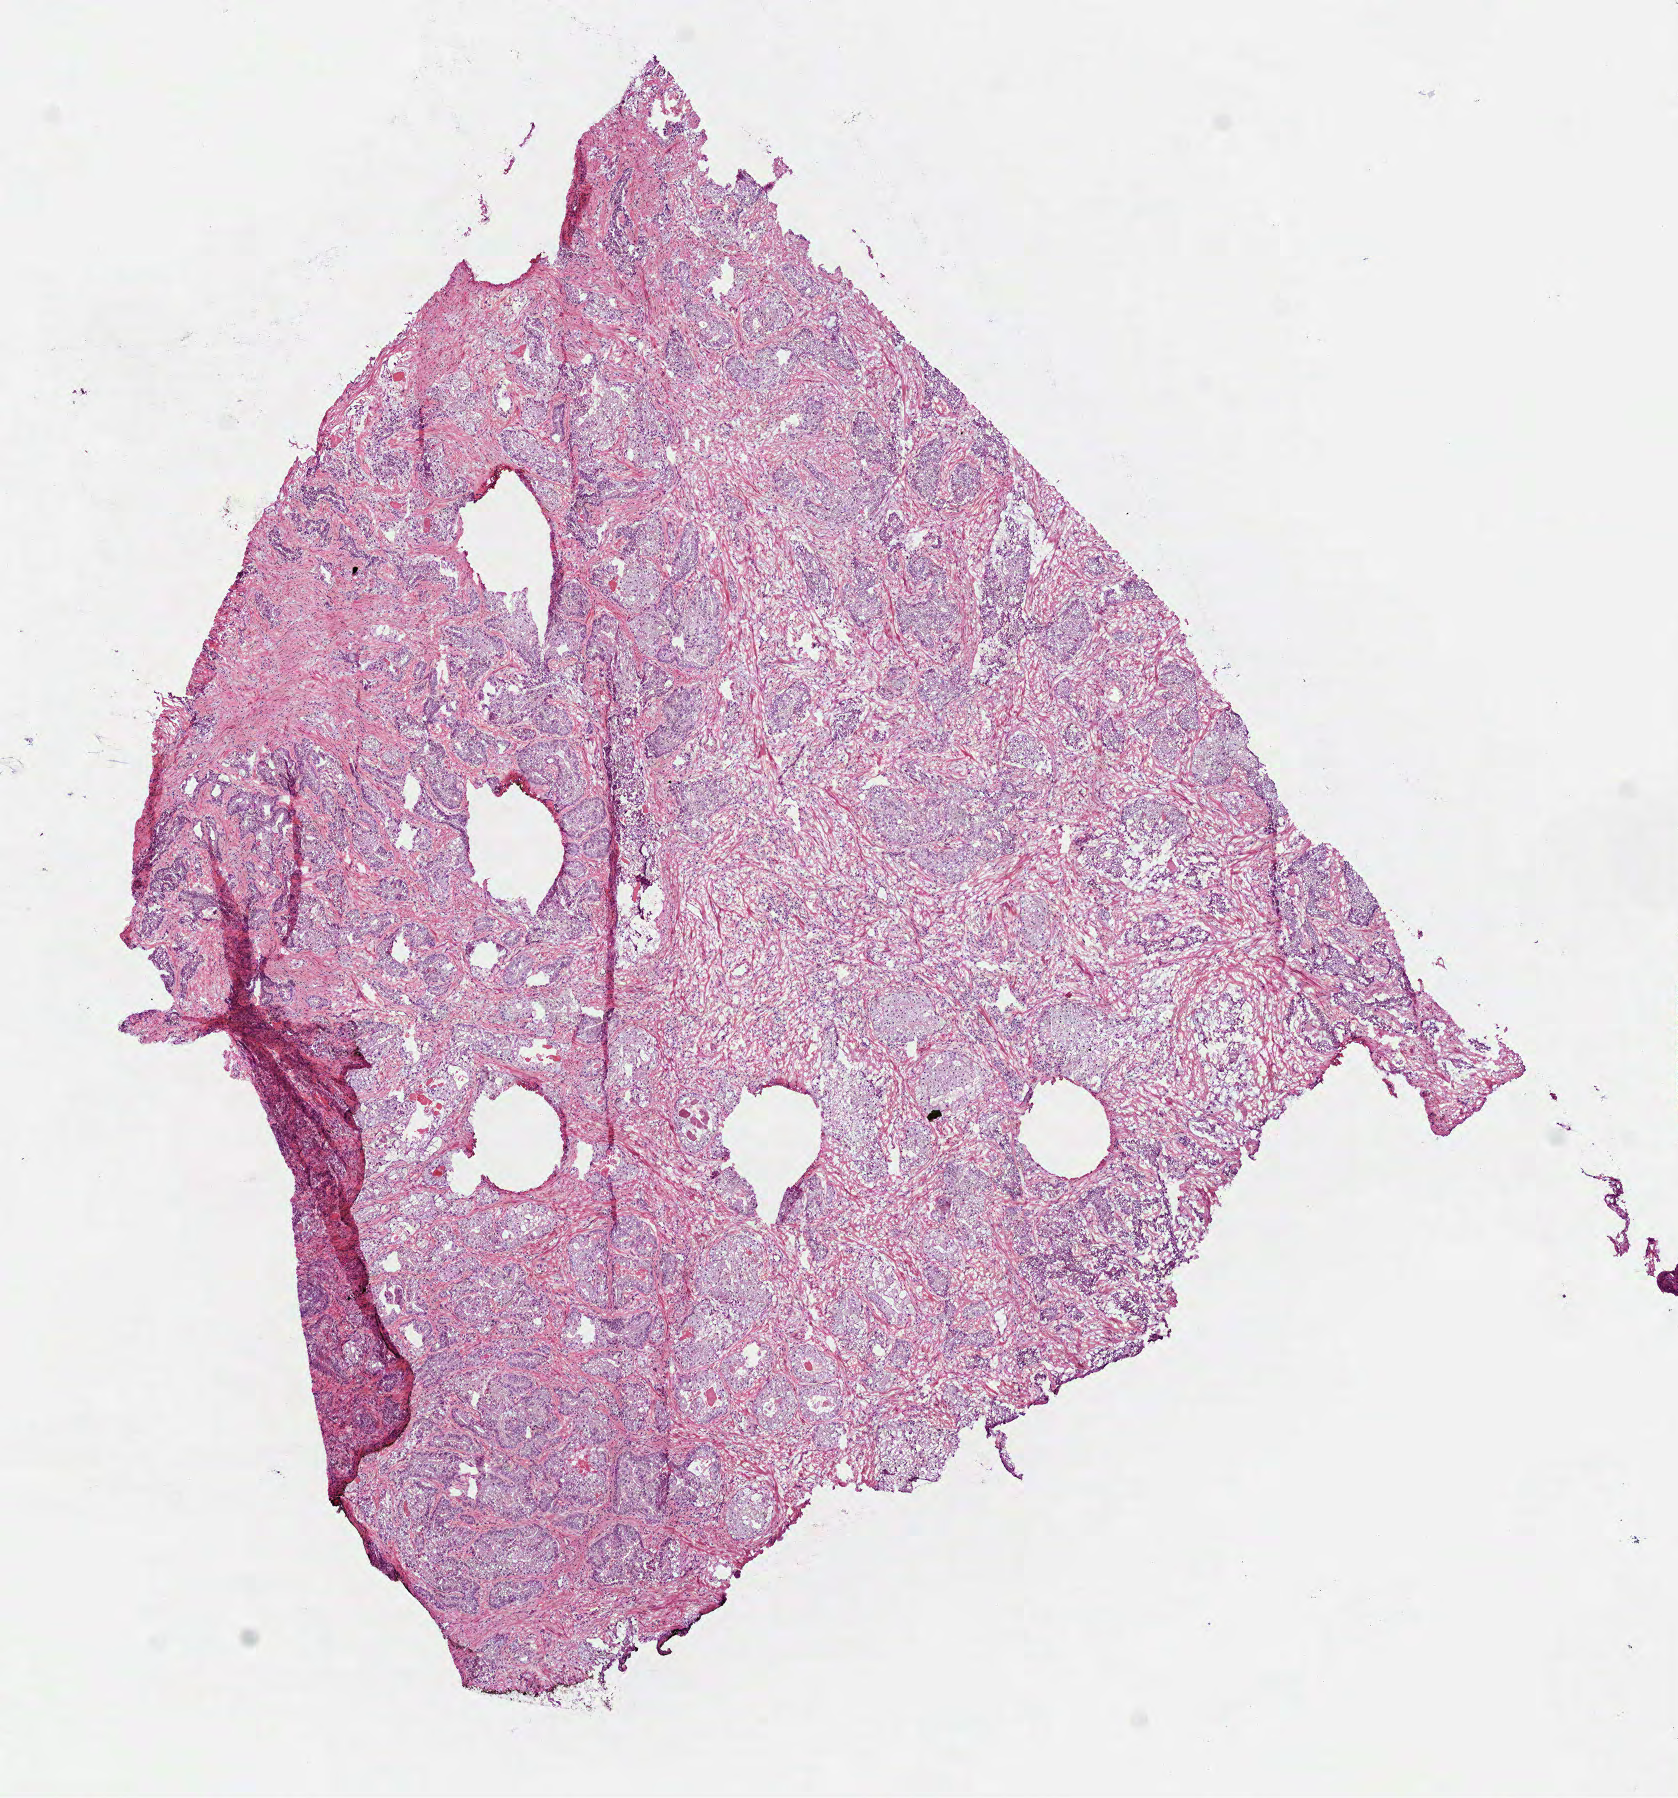
Whole-slide histology image, Hematoxylin and eosin (H&E) stained, a low-resolution overview of the entire scanned area, about 6.8 x 7.3 mm (acquisition: 40x scan); frozen section from the top of the tissue portion; prostate, primary tumour sample. Male, age 62 years at initial diagnosis. Gleason score: 9 (4+5). Pathologist review of this section (percent, as recorded): tumour cells 70%, tumour nuclei 70%, normal cells 10%, stromal cells 20%, necrosis 0%.
- pathologic diagnosis: Acinar cell carcinoma (prostate gland)